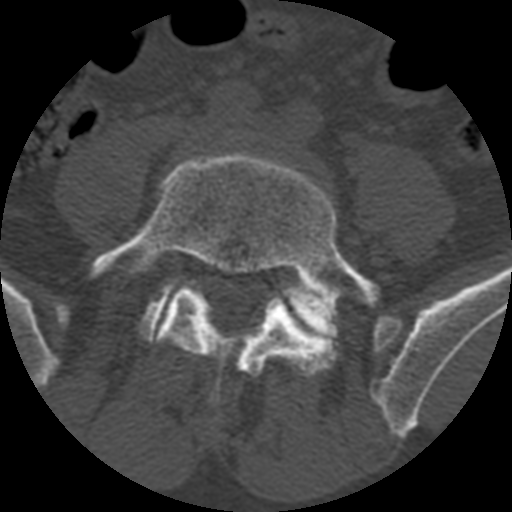
CT including the spine, one axial slice. Slice 256 of 399 in the series (ordered by position). 120 kVp. Bone window (W 1800 / L 400 HU). 1.25 mm slice thickness. 512 × 512 image matrix, field of view 160 × 160 mm. Patient age 71 years. Case-level facts recorded for this patient, not image findings: primary cancer: prostate.
Outlined on this slice (semi-automatic segmentation, software-assisted and operator-edited):
- L5 vertebra: bounding box [x1, y1, x2, y2] px = [87, 151, 380, 405]